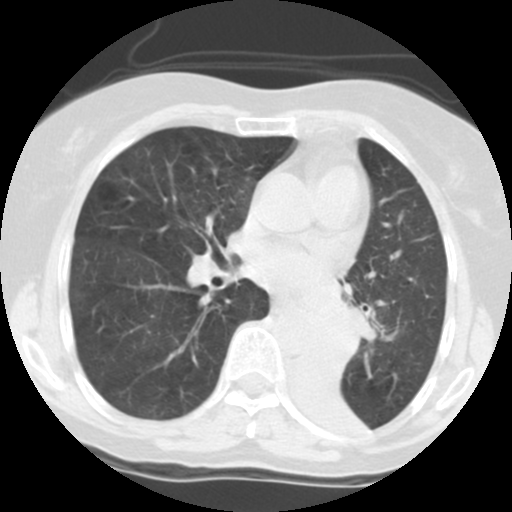
Chest CT (low-dose screening protocol), one axial image. Third annual screen. Lung window (W 1500 / L -600 HU). Slice 66 of 113 in the series. 512 × 512 image matrix, field of view 280 × 280 mm. Female participant, aged 56 years at enrolment. Former smoker at enrolment.
• Expert reader's lesion annotation, bounding box [x1, y1, x2, y2] px = [301, 303, 368, 361].
• Screening reader's record for this exam: no non-calcified nodule ≥4 mm recorded.
• Official screen result: positive, other.
• Lung cancer was diagnosed 9 days after this screen: squamous cell carcinoma, NOS, left main stem bronchus, poorly differentiated (G3), stage IIIA (AJCC 6th edition).